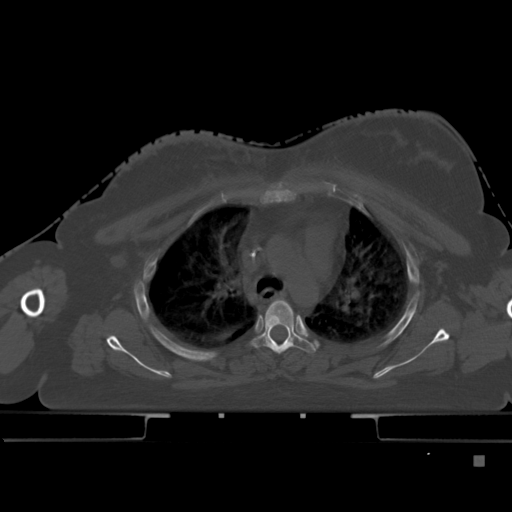
CT including the spine, one axial slice; position 335 of 495 along the scan axis; bone window (W 1800 / L 400 HU); 1.5 mm slice thickness; 512 × 512 image matrix. Female patient, age 33 years. Case-level facts recorded for this patient, not image findings: primary cancer: breast.
Outlined on this slice (semi-automatic segmentation, software-assisted and operator-edited):
- T4 vertebra: bounding box [x1, y1, x2, y2] px = [253, 299, 318, 355]